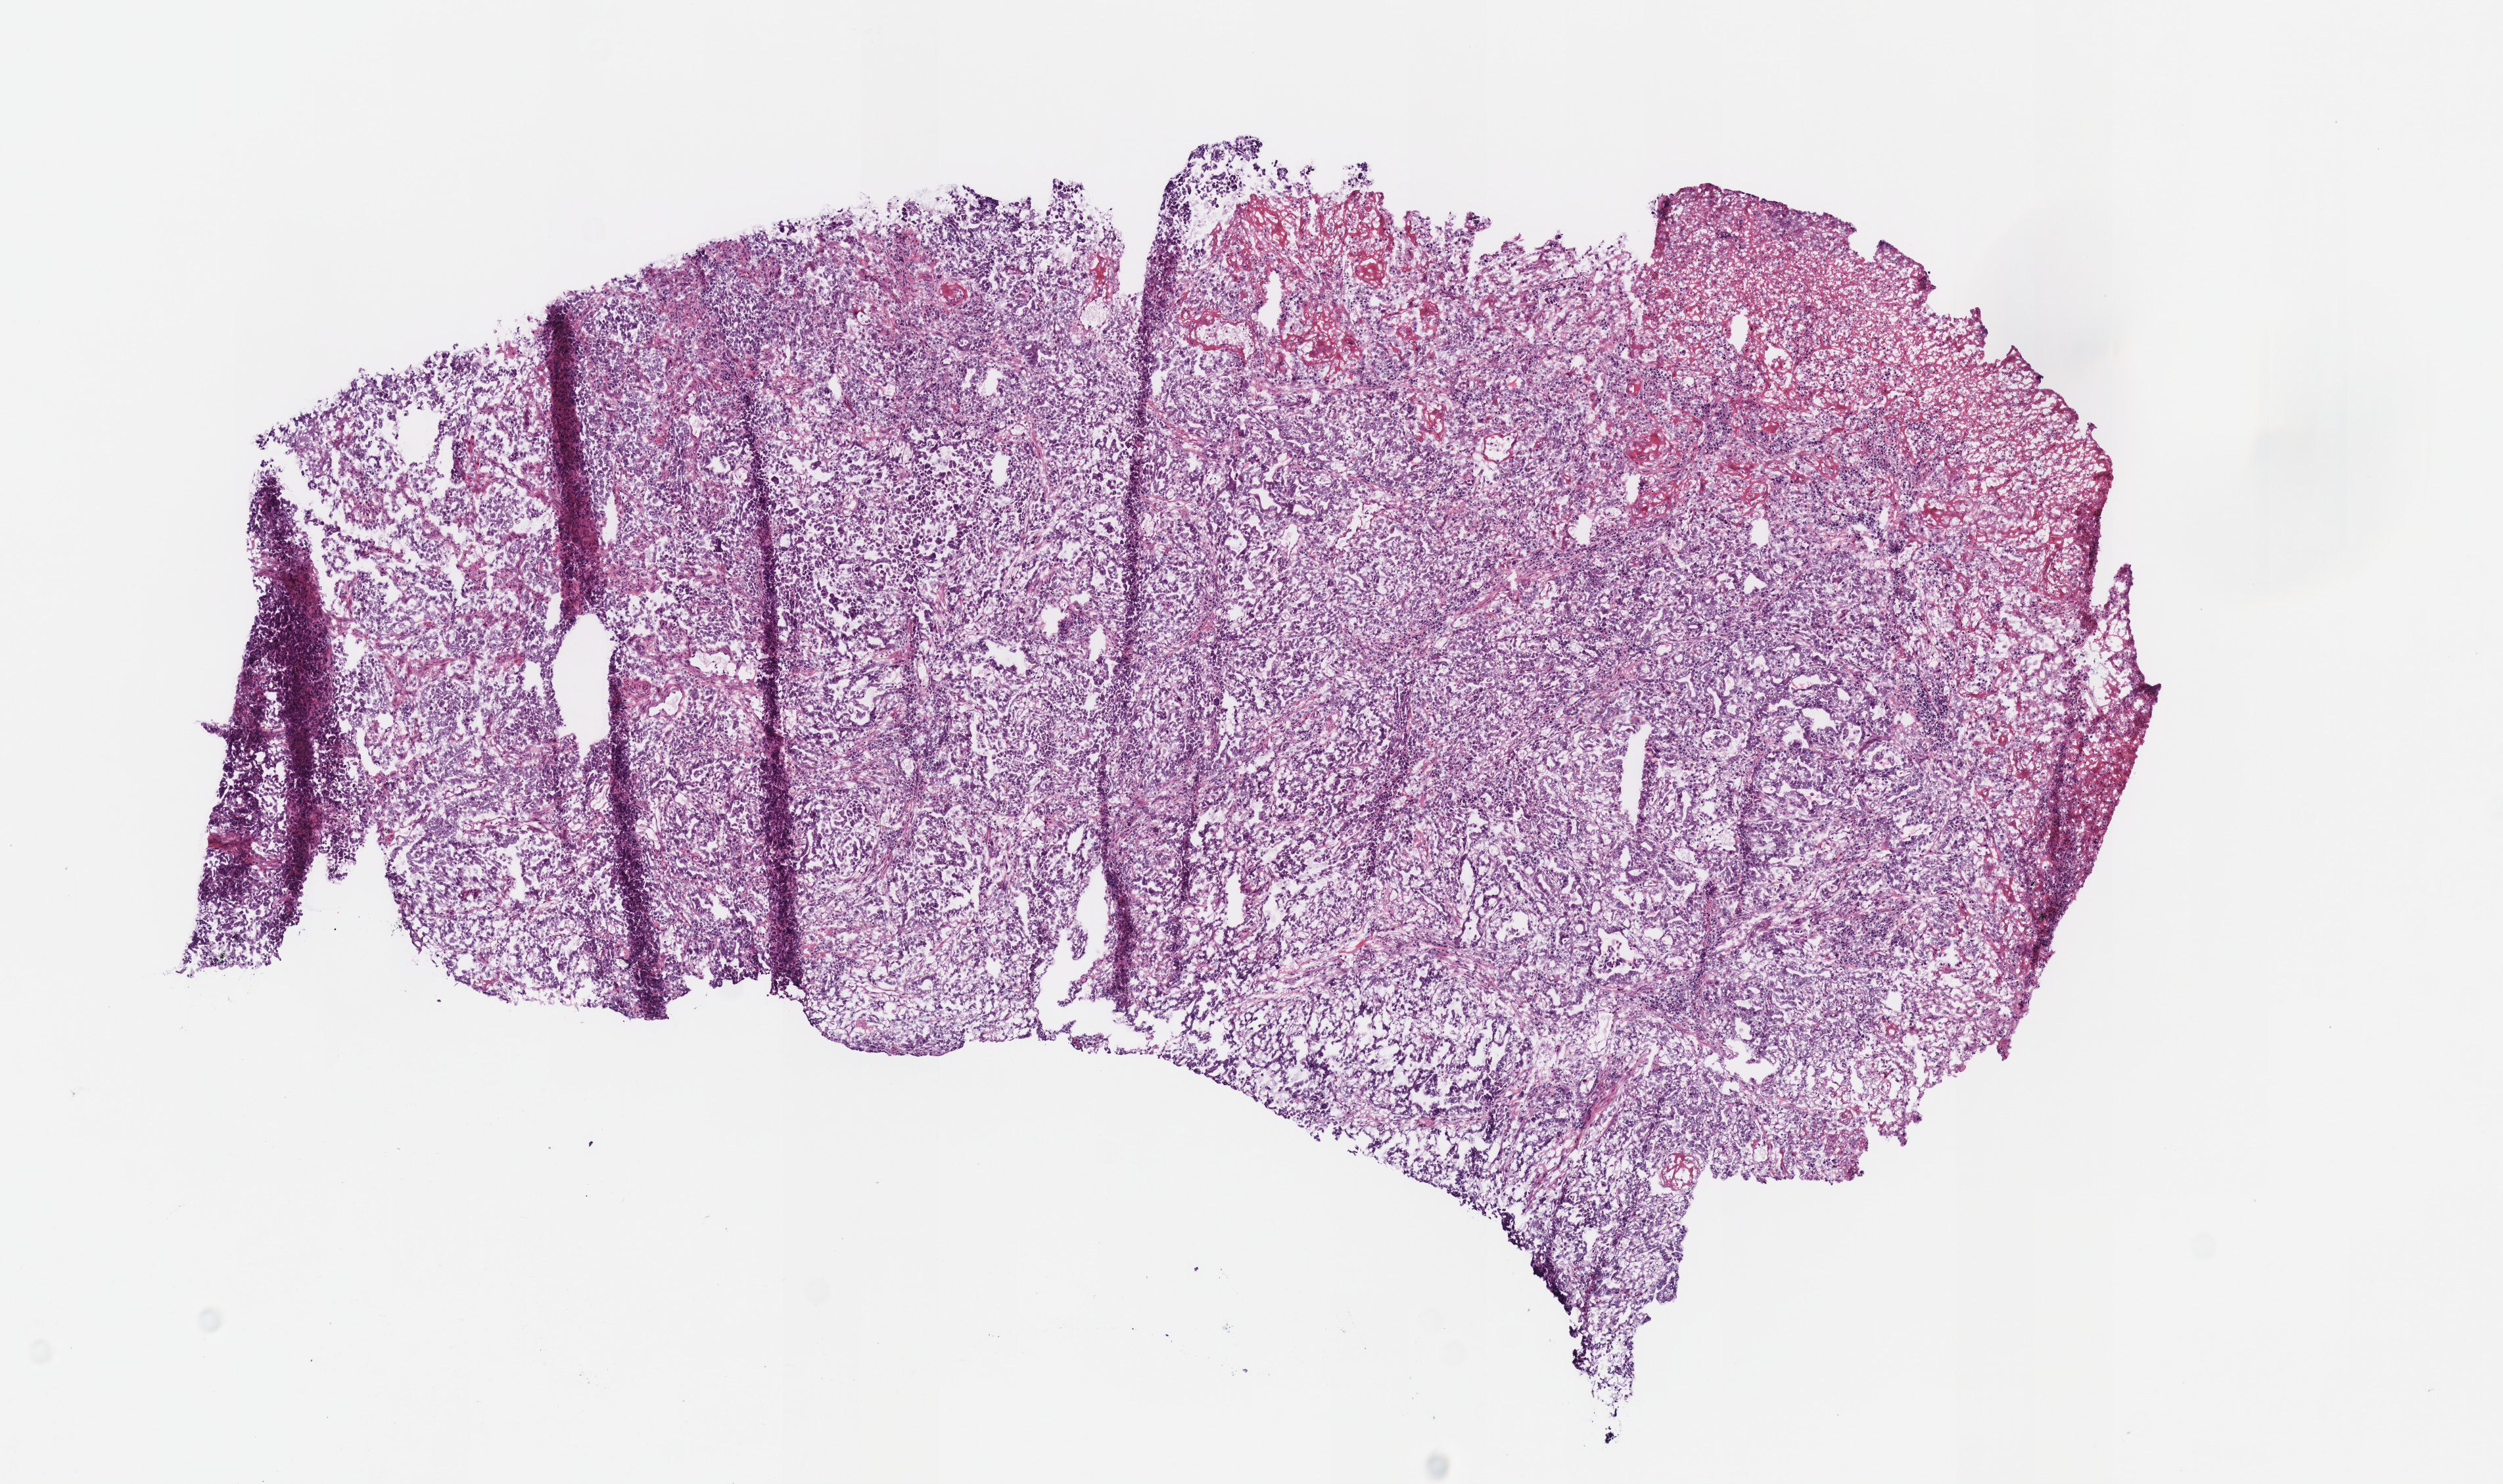
H&E-stained whole-slide image, shown as a low-resolution overview of the whole scanned area (about 7.5 x 4.4 mm, acquisition: 40x scan), frozen section from the top of the tissue portion, primary tumour sample from the stomach. Male patient; age at initial diagnosis 66 years.
Histologic diagnosis: Tubular adenocarcinoma (body of stomach).